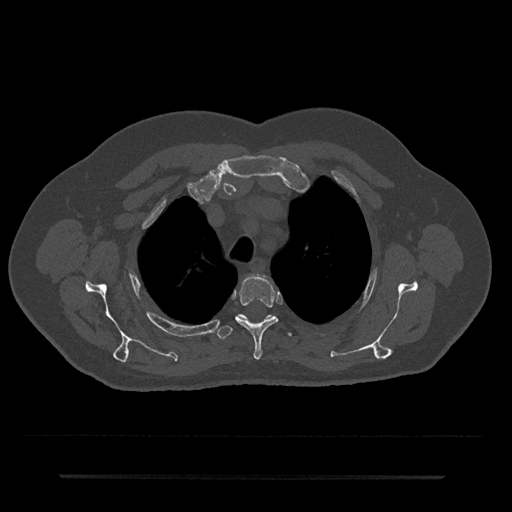
CT including the spine, one axial slice; slice 560 of 797 in the series (ordered by position); reconstruction kernel Br40s/3; bone window (W 1800 / L 400 HU); 0.5 mm slice thickness; 512 × 512 image matrix. Patient: male, 69 years. Case-level facts recorded for this patient, not image findings: primary cancer: prostate.
Structures marked on this image (semi-automatic segmentation, software-assisted and operator-edited):
- T3 vertebra: bounding box [x1, y1, x2, y2] px = [235, 275, 278, 360]
- T4 vertebra: [217, 314, 292, 339]